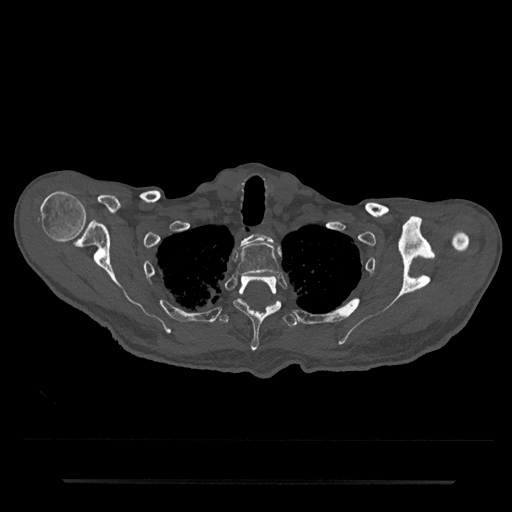
CT including the spine, one axial slice; position 663 of 797 along the scan axis; 120 kVp; bone window (W 1800 / L 400 HU); 0.5 mm slice thickness; 512 × 512 image matrix, field of view 427 × 427 mm. Patient: male, 74 years. From the clinical record (not read from this slice): primary cancer: prostate.
Annotated regions visible in this slice (semi-automatically segmented with operator editing):
- T1 vertebra: box from (x=241, y=234) to (x=274, y=244) px
- T2 vertebra: (x=236, y=243)–(x=279, y=276)
- T3 vertebra: (x=233, y=275)–(x=282, y=352)
- T4 vertebra: (x=217, y=301)–(x=298, y=329)